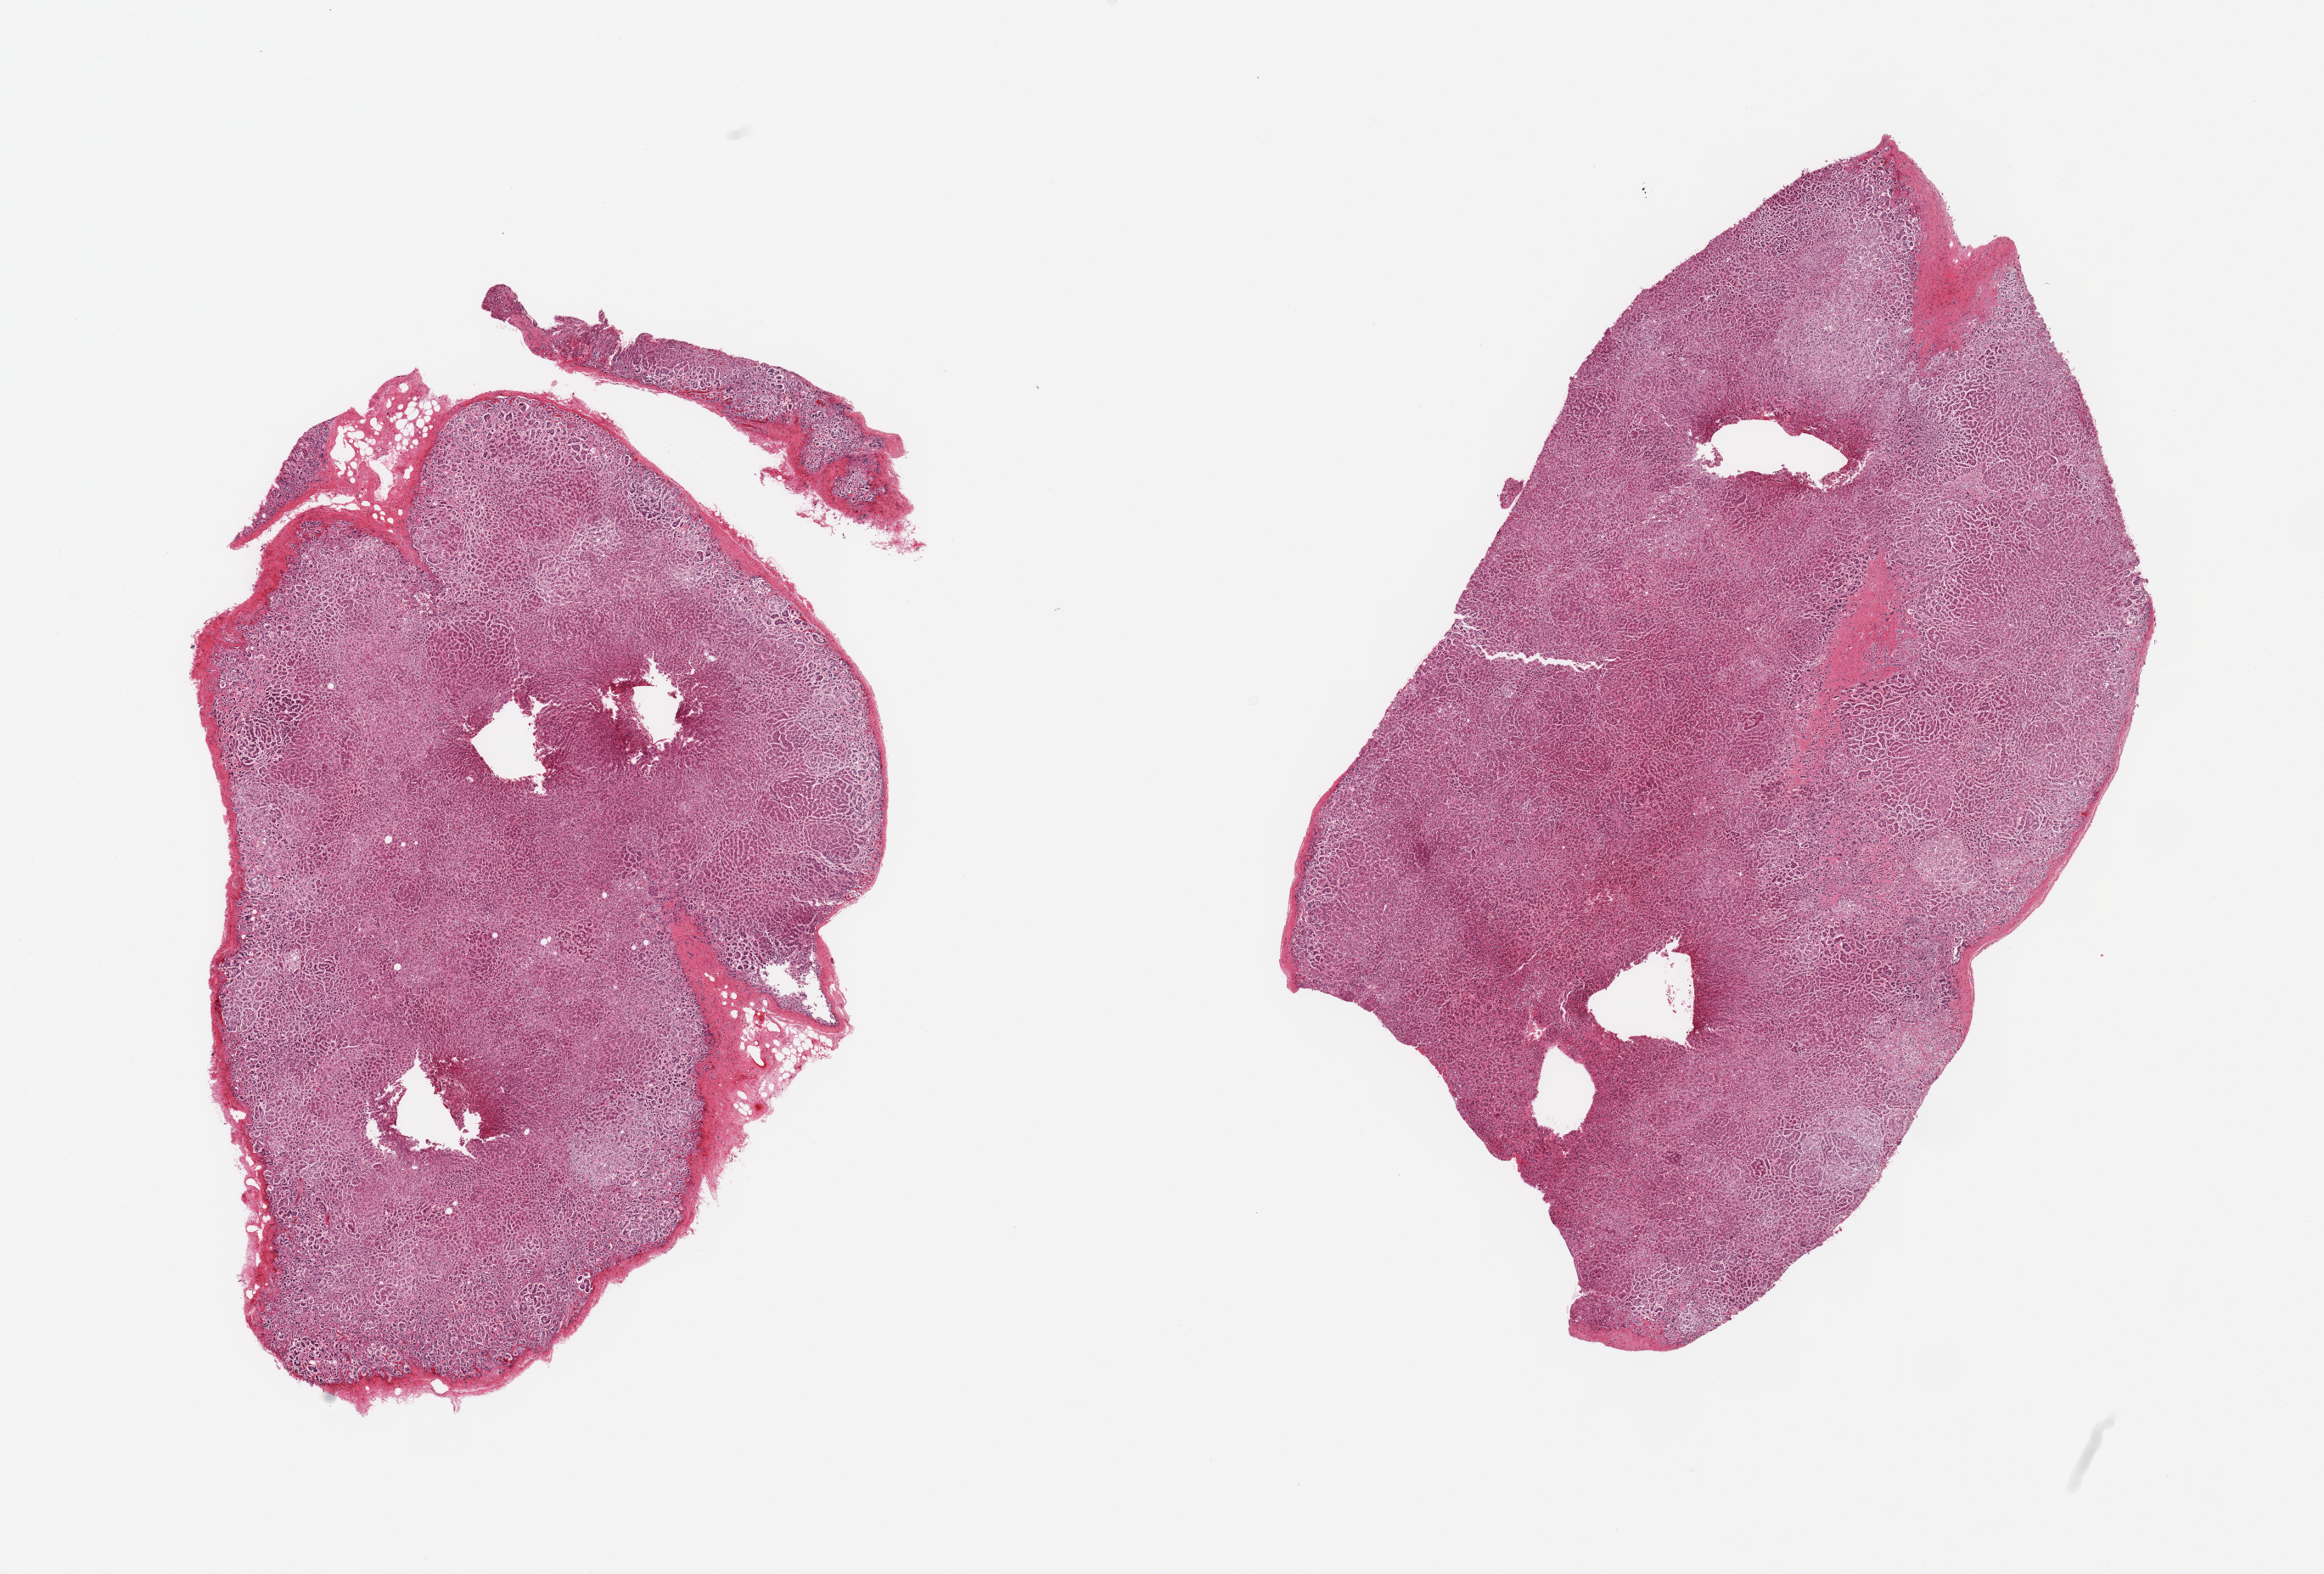
Whole-slide image, haematoxylin and eosin stain — low-resolution overview of the scanned area, about 21.7 x 14.7 mm; PAXgene-fixed paraffin-embedded (PFPE) section; target tissue: adrenal gland; tissue donor sample. Donor: male.
Pathologist's review note for this sample: 2 pieces, cortex, advanced autolysis.